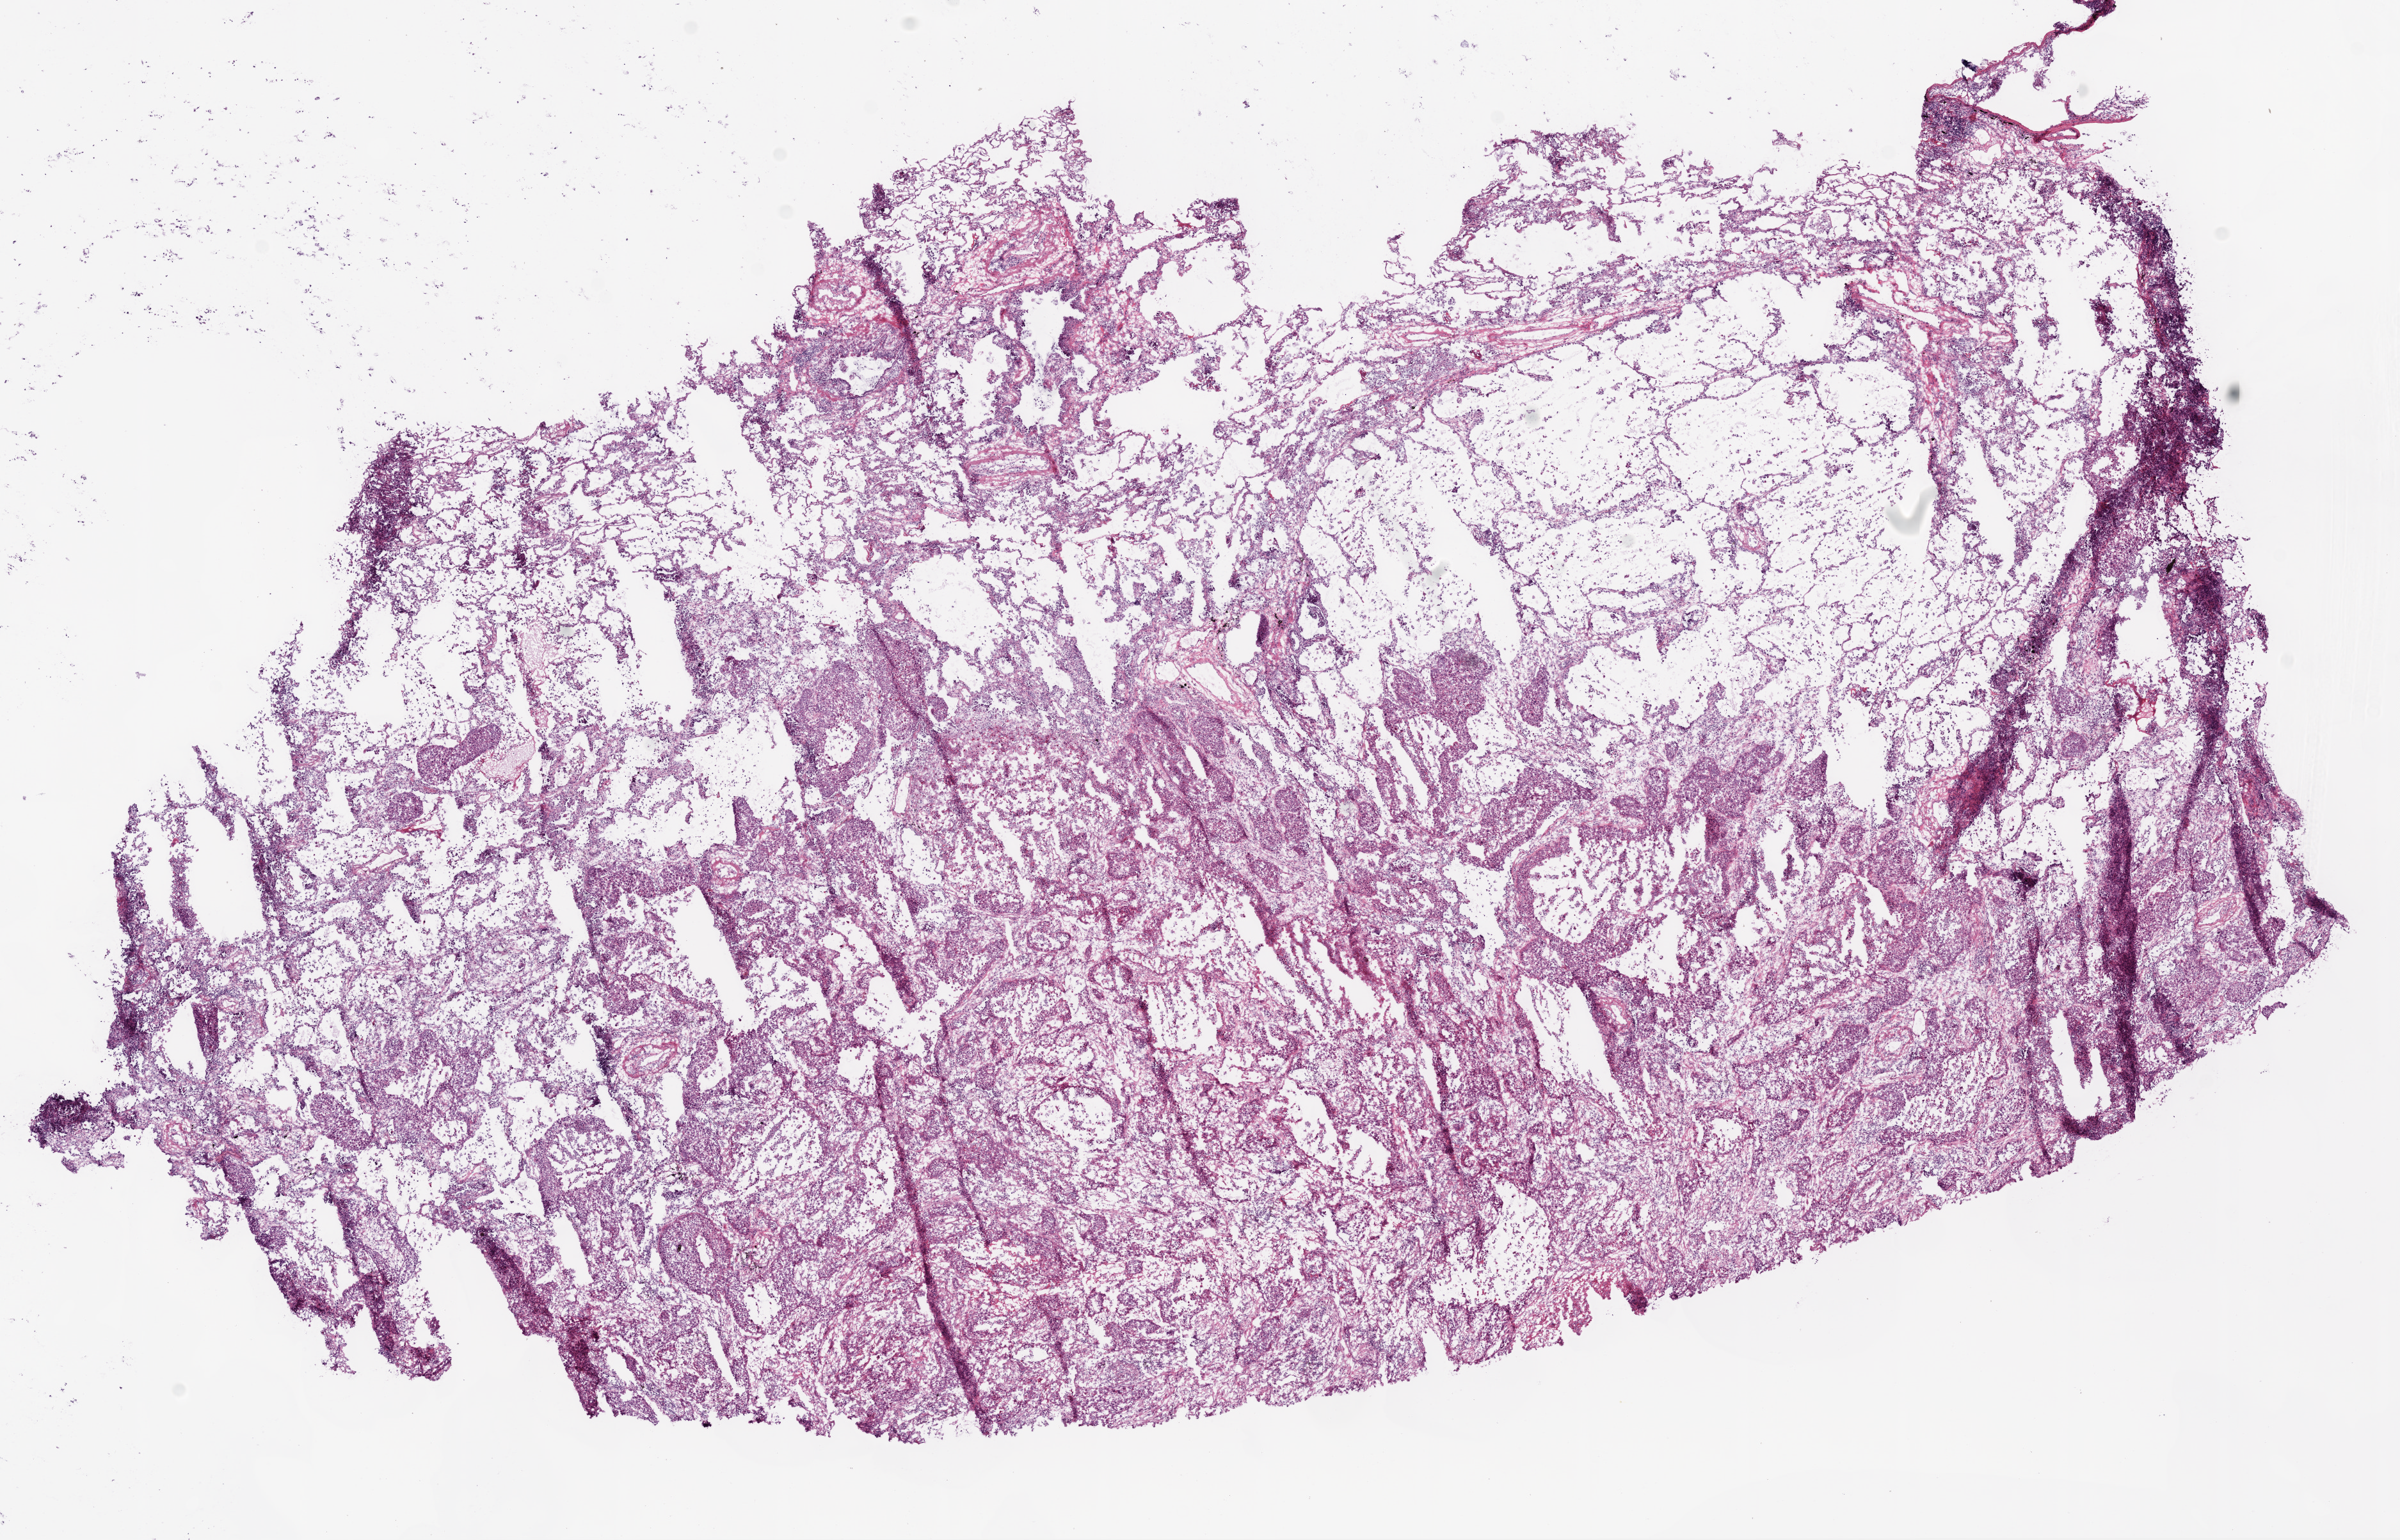
Digitized Hematoxylin and eosin (H&E) stained tissue section (whole slide) — whole scanned area (about 15.0 x 9.7 mm) shown as a low-resolution overview; frozen section; sample: primary tumour, lung. Female patient; age at initial diagnosis 81 years. Slide review estimates, as recorded: tumour cells 75%, tumour nuclei 85%, normal cells 15%, stromal cells 5%, necrosis 5%. Infiltration values recorded for this section: lymphocyte infiltration 3%, monocyte infiltration 1%, neutrophil infiltration 4%.
- laterality: left
- diagnosis: Squamous cell carcinoma, NOS (lower lobe, lung)
- TNM: T2 N0 M0
- AJCC pathologic stage: IB